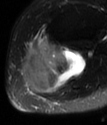
MRI of an extremity soft-tissue mass, one axial slice; position 44 of 78 along the scan axis; T2-weighted fat-saturated; MR volume resampled by the dataset authors to the PET/CT grid (not the native acquisition matrix); 3.27 mm slice thickness; 107 × 125 image matrix, field of view 104 × 122 mm. Female patient. Case-level facts recorded for this patient, not image findings: histological type: extraskeletal high grade osteogenic sarcoma; grade: high; site of the primary tumour: left calf.
Annotated regions visible in this slice (expert contour drawn on MRI and transferred to this co-registered scan by the dataset authors):
- gross tumour volume (mass): bounding box [x1, y1, x2, y2] px = [23, 40, 86, 94]